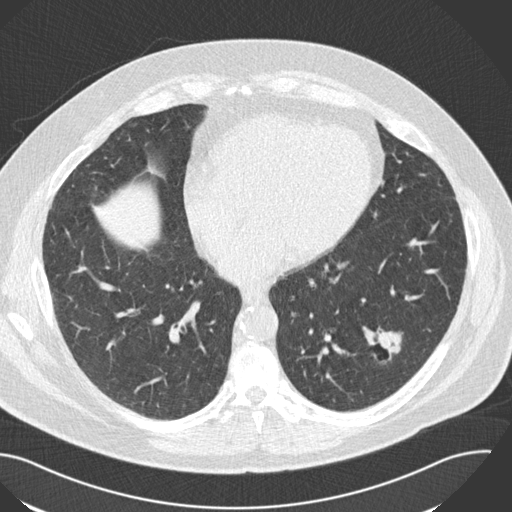
Low-dose screening chest CT, one axial slice. Reconstruction kernel B30f. Lung window (W 1500 / L -600 HU). 2 mm slice thickness. 512 × 512 image matrix, field of view 394 × 394 mm.
Annotated regions visible in this slice (expert manual segmentation):
- lesion 1 (tumor, lower lobe of left lung): bounding box [x1, y1, x2, y2] px = [377, 328, 401, 360]